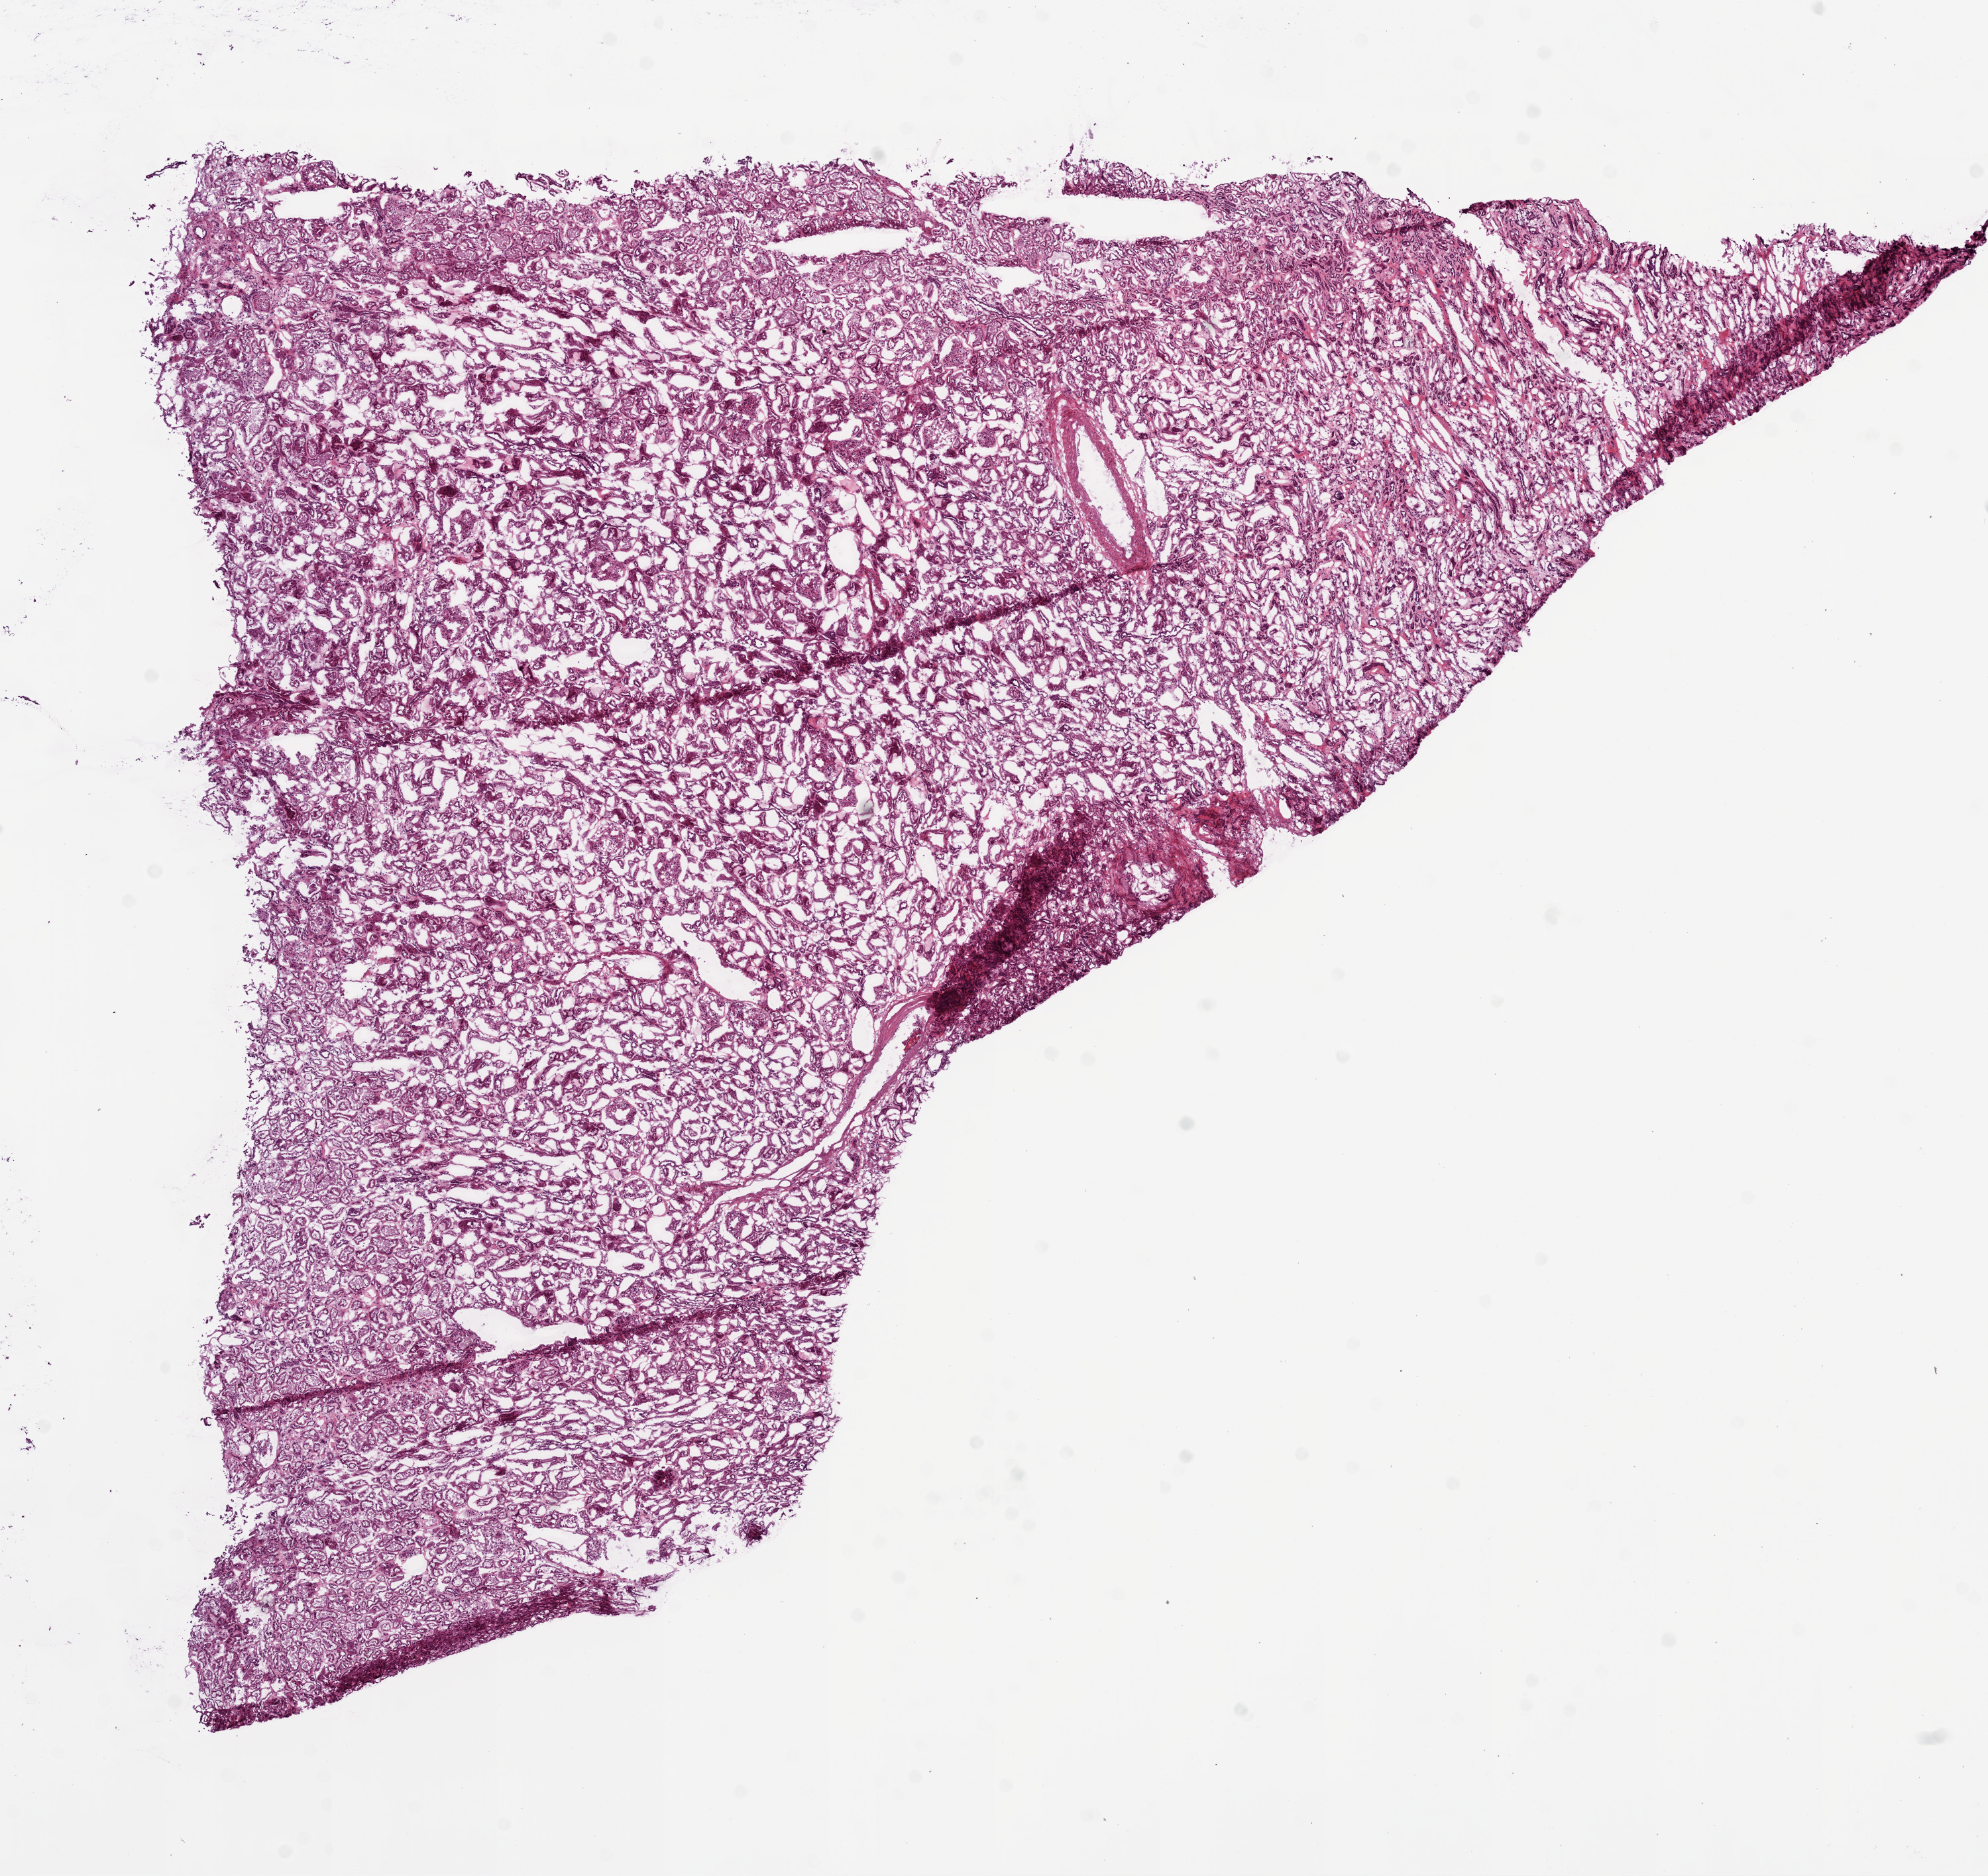
Whole-slide histology image, H&E-stained — whole scanned area (about 12.0 x 11.4 mm, slide scanned at 20x) shown as a low-resolution overview, frozen section from the bottom of the tissue portion, solid tissue normal (non-tumour tissue) sample from the kidney. Female, age 77 years at initial diagnosis.
This section: solid tissue normal sample (biorepository sample class). Patient diagnosis: Clear cell adenocarcinoma, NOS.